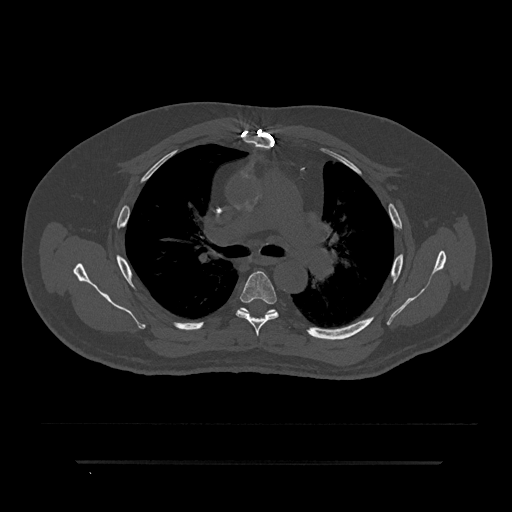
CT including the spine, one axial slice; position 565 of 797 along the scan axis; reconstruction kernel Br40s/3; bone window (W 1800 / L 400 HU); 512 × 512 image matrix, field of view 464 × 464 mm. Patient: male, 59 years. From the clinical record (not read from this slice): primary cancer: bile ducts; vertebrae with lytic lesions (as recorded): T10.
Outlined on this slice (semi-automatically segmented with operator editing):
- T5 vertebra: bounding box [x1, y1, x2, y2] px = [236, 271, 279, 336]
- T6 vertebra: [239, 308, 274, 315]